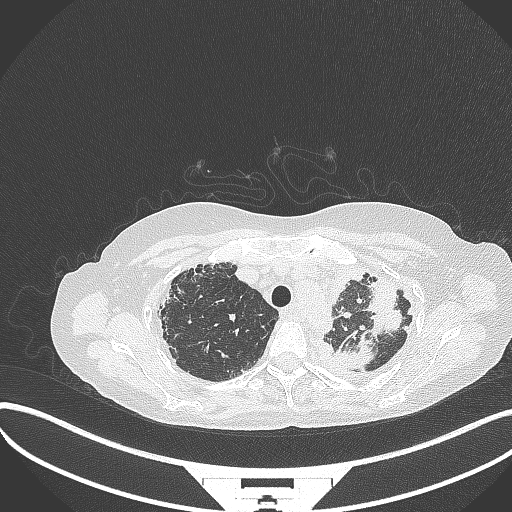
Chest CT, one axial slice; slice 274 of 373 in the series (ordered by position); reconstruction kernel B70f; lung window (W 1500 / L -600 HU); 512 × 512 image matrix, field of view 400 × 400 mm. Patient: female, 56 years. Case-level facts recorded for this patient, not image findings: clinical TNM (as recorded): T1 N0 M0.
Annotated regions visible in this slice (bounding box drawn by a radiologist):
- lung tumour (recorded histology: adenocarcinoma): bounding box <336,331,378,370> (left, top, right, bottom; pixels)
- lung tumour (recorded histology: adenocarcinoma): <360,273,409,335>